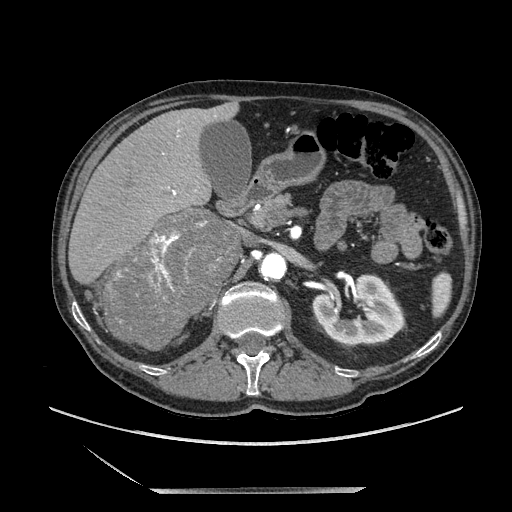
Contrast-enhanced abdominal CT, one axial slice. Slice 114 of 243 in the series (ordered by position). Soft-tissue window (W 400 / L 40 HU). 512 × 512 image matrix. Male patient. Case-level facts recorded for this patient, not image findings: diagnosis: adrenocortical carcinoma; tumour side: right adrenal; tumour size at pathology: 16 cm; Ki-67 index: 17 %; stage (as recorded): 3.
Structures marked on this image (semi-automatic segmentation, software-assisted and operator-edited):
- mass: box from (x=108, y=210) to (x=233, y=349) px